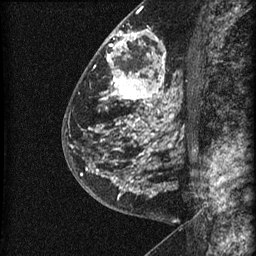
Breast MRI (dynamic contrast-enhanced), one sagittal slice. Slice 31 of 60 in the series (ordered by position). Dynamic contrast-enhanced series, image 2 of 3 at this slice position (ordered by acquisition). 1.5 T. TE 4.2 ms, TR 22.7 ms. 256 × 256 image matrix, field of view 180 × 180 mm. Patient: female, 48 years. From the clinical record (not read from this slice): setting: breast cancer imaged before/during neoadjuvant chemotherapy; receptor status: triple-negative.
Outlined on this slice (semi-automatically segmented with operator editing):
- analysis volume of interest (the breast-tissue region the enhancement analysis was run in; not a lesion): bounding box [x1, y1, x2, y2] px = [81, 23, 186, 202]
- tumour enhancement mask (voxels above the 90 % enhancement threshold inside the analysis volume of interest): [81, 30, 173, 197]